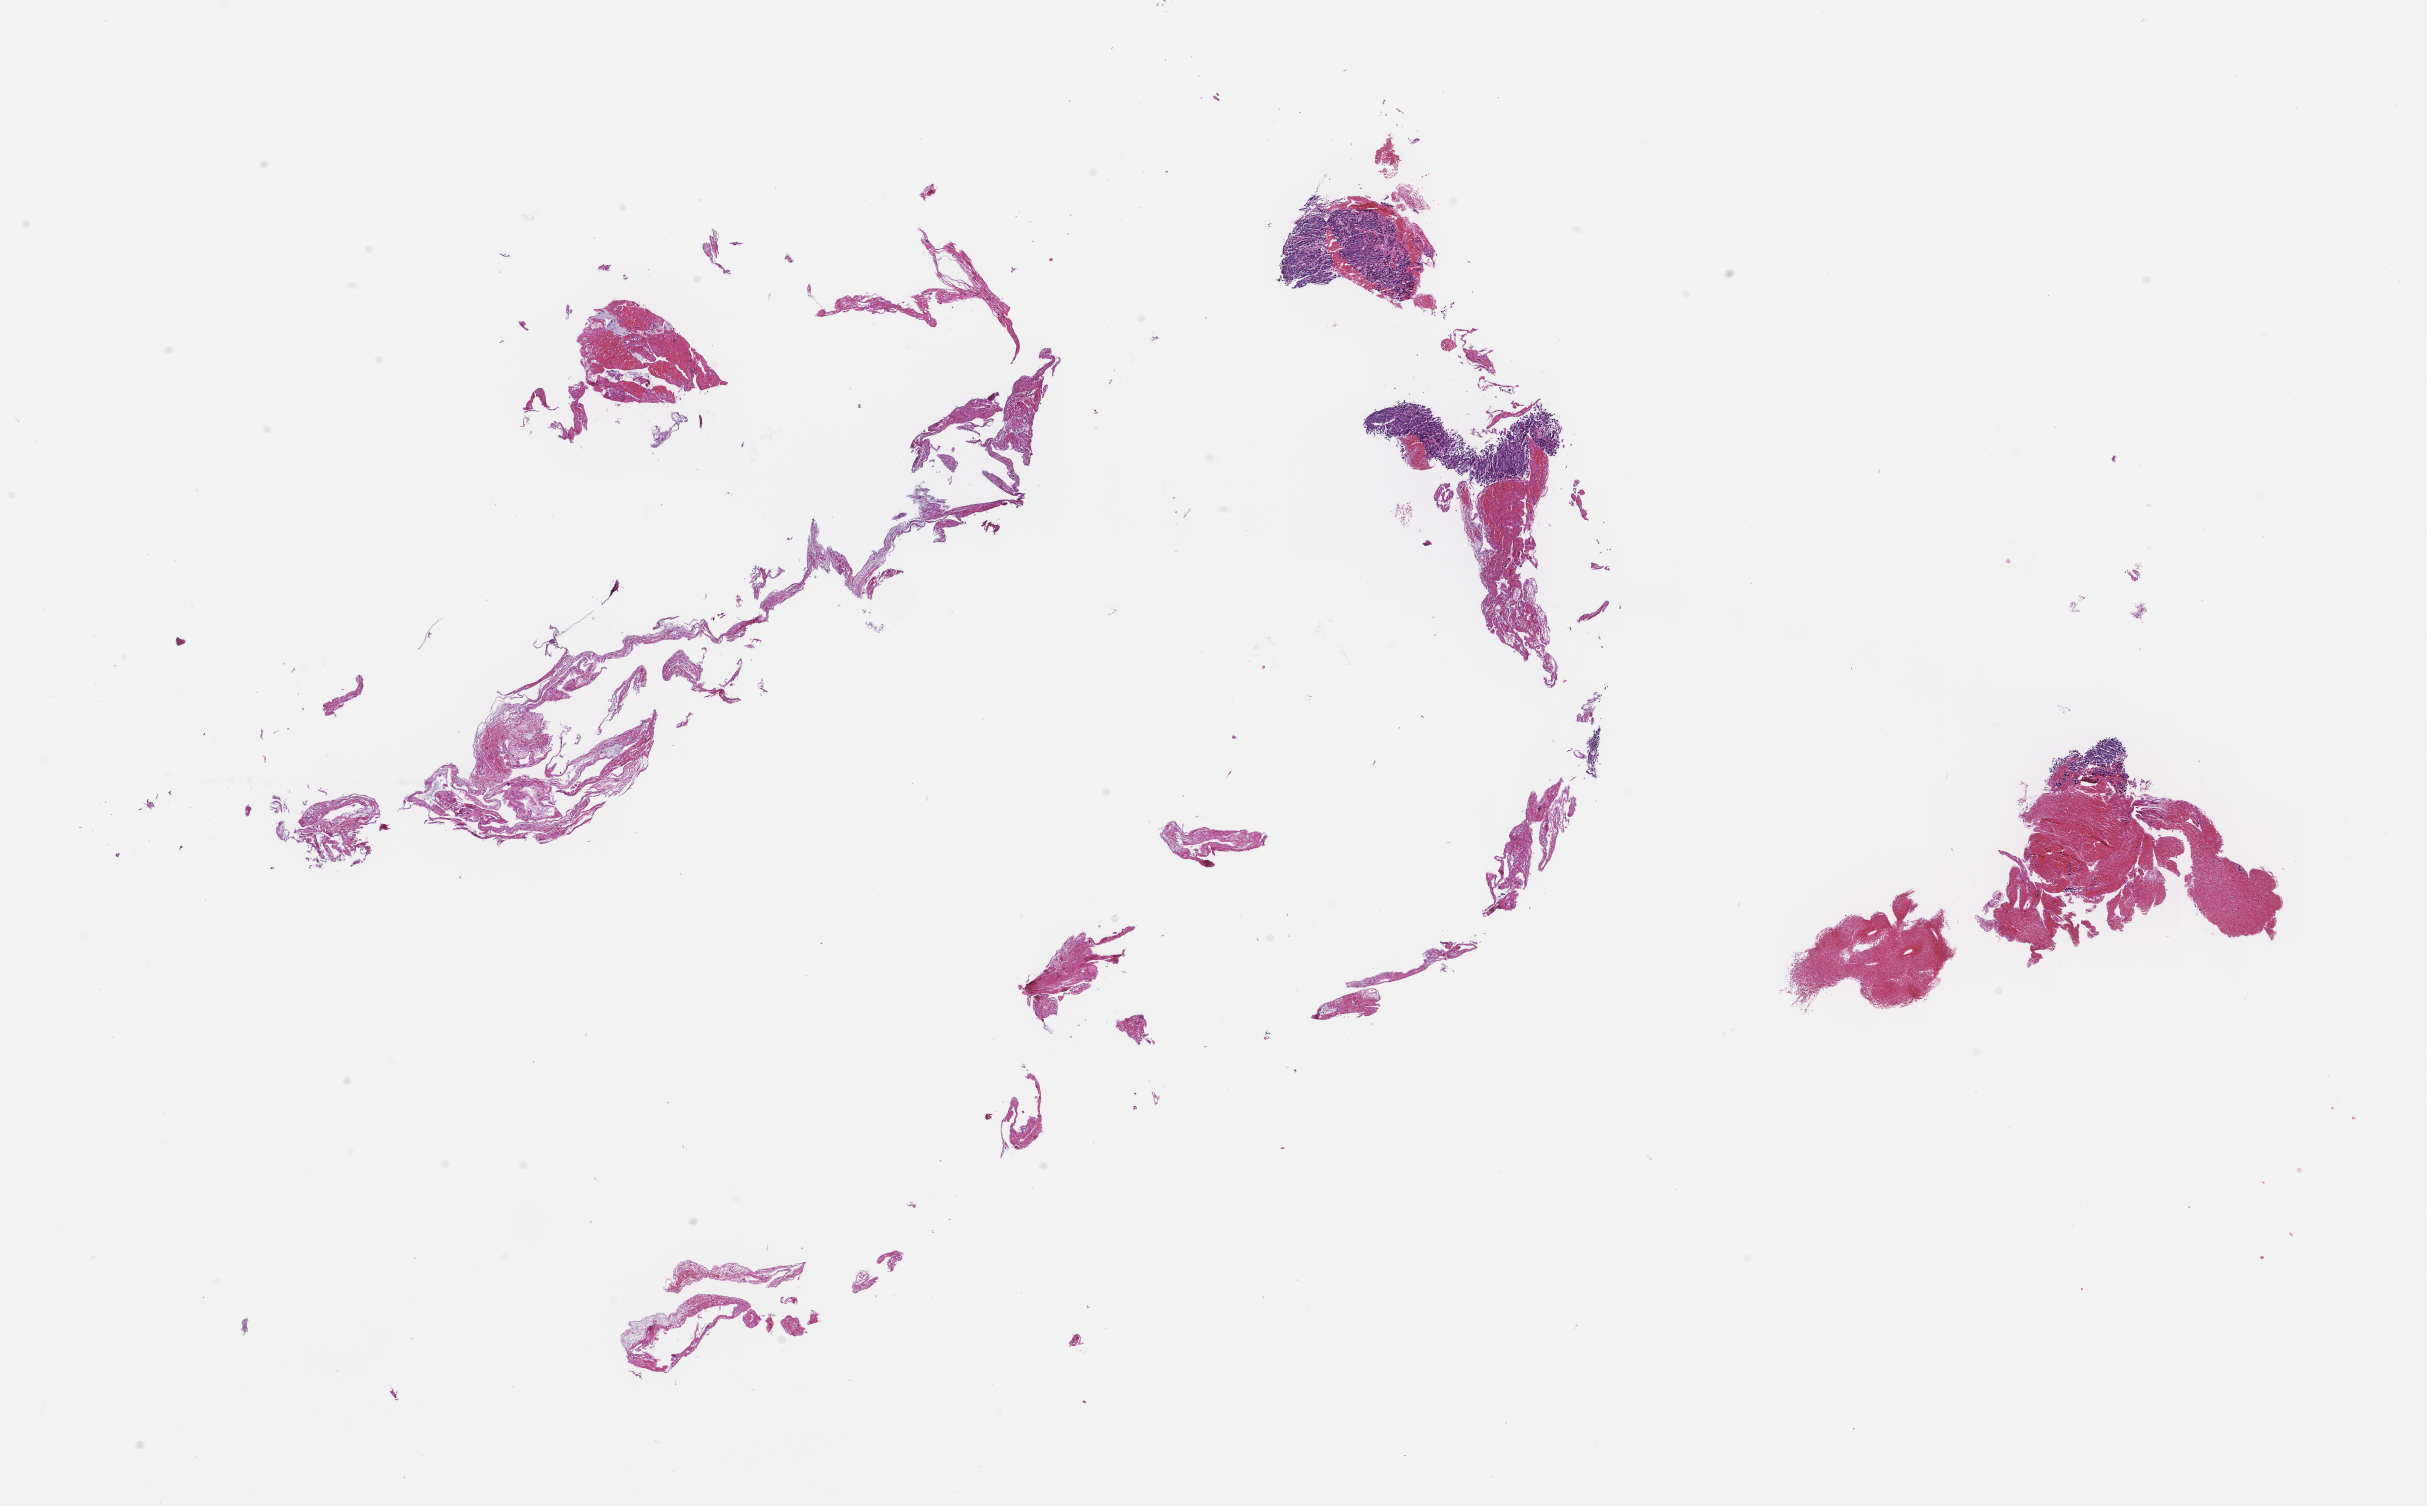
Hematoxylin and eosin (H&E) whole-slide image — whole scanned area (about 19.6 x 12.2 mm) shown as a low-resolution overview. Formalin-fixed paraffin-embedded section. Specimen time point: collected at disease progression. Patient sex: female.
This section: metastatic tumor tissue. Patient diagnosis (primary): Melanoma.